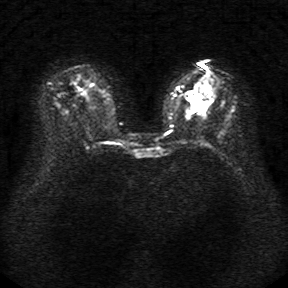
Breast MRI, one axial slice; slice 15 of 34 in the series (ordered by position); diffusion-weighted series; image 2 of 4 stored at this slice position (different b-values; order by instance number); 1.5 T; 5 mm slice thickness; 288 × 288 image matrix, field of view 340 × 340 mm. Female patient.
Annotated regions visible in this slice (expert manual segmentation):
- tumour on diffusion-weighted imaging: bounding box [x1, y1, x2, y2] px = [190, 95, 207, 110]